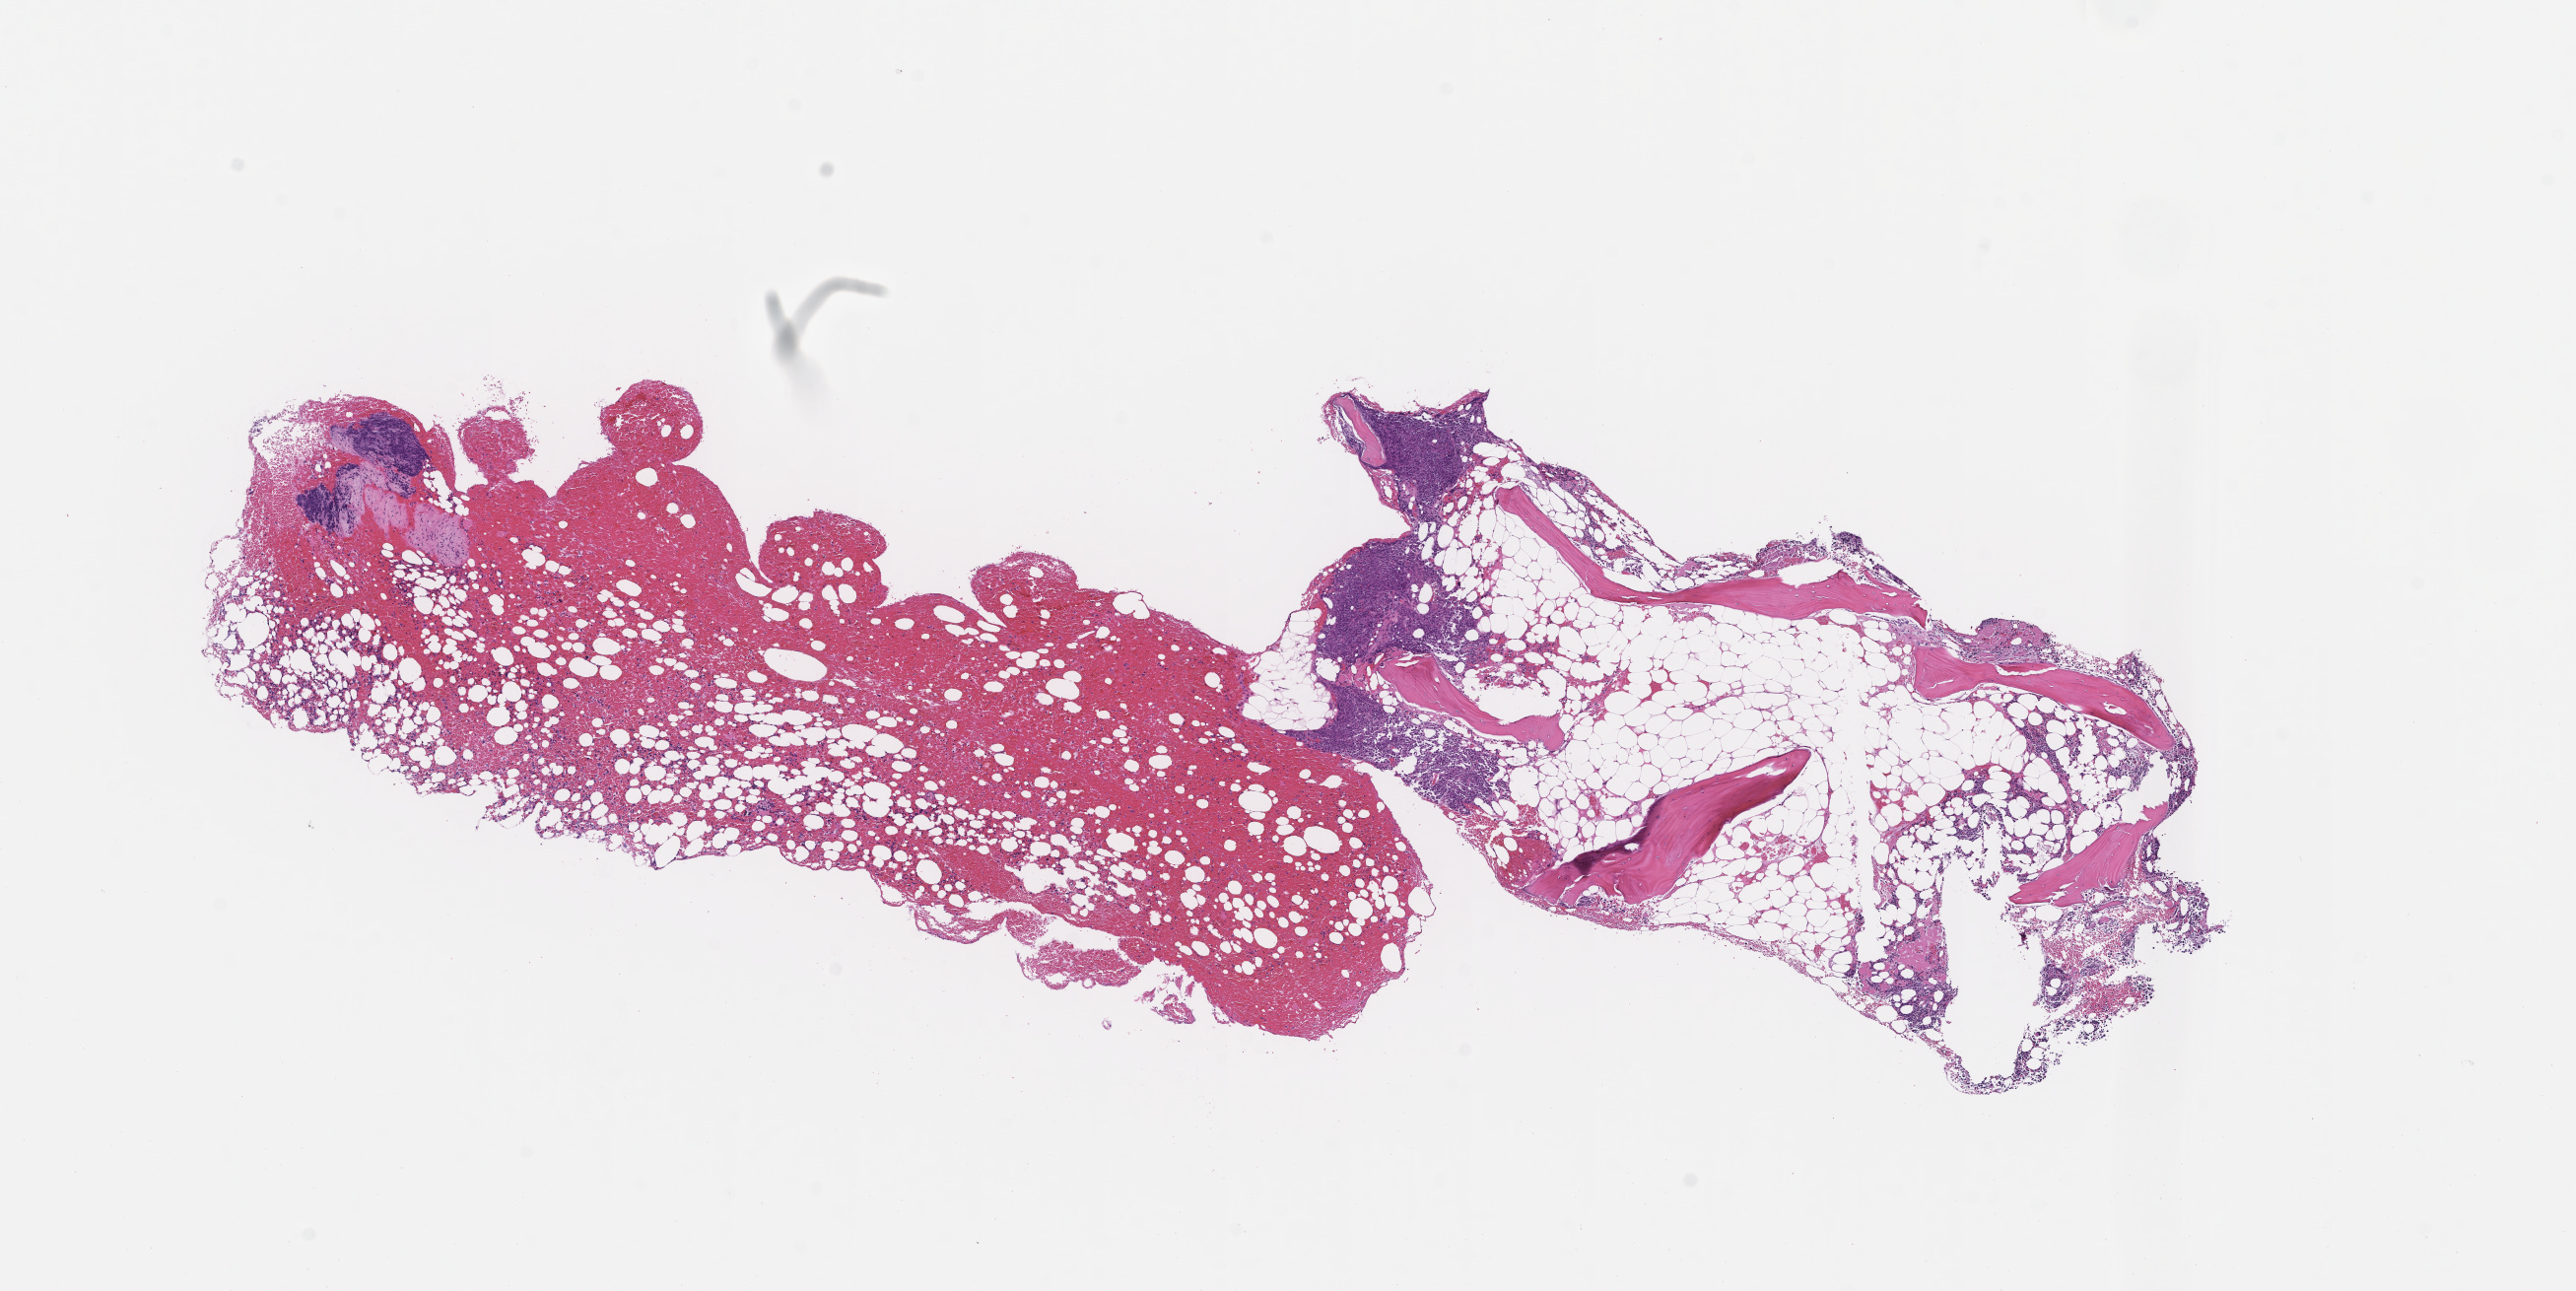
Digitized haematoxylin and eosin-stained section, shown as a low-resolution overview of the whole scanned area (about 10.6 x 5.3 mm); formalin-fixed, paraffin-embedded (FFPE) tissue; tissue site: bone marrow. Patient: male.
• this section: primary tumour tissue
• diagnosis: Plasma Cell Myeloma